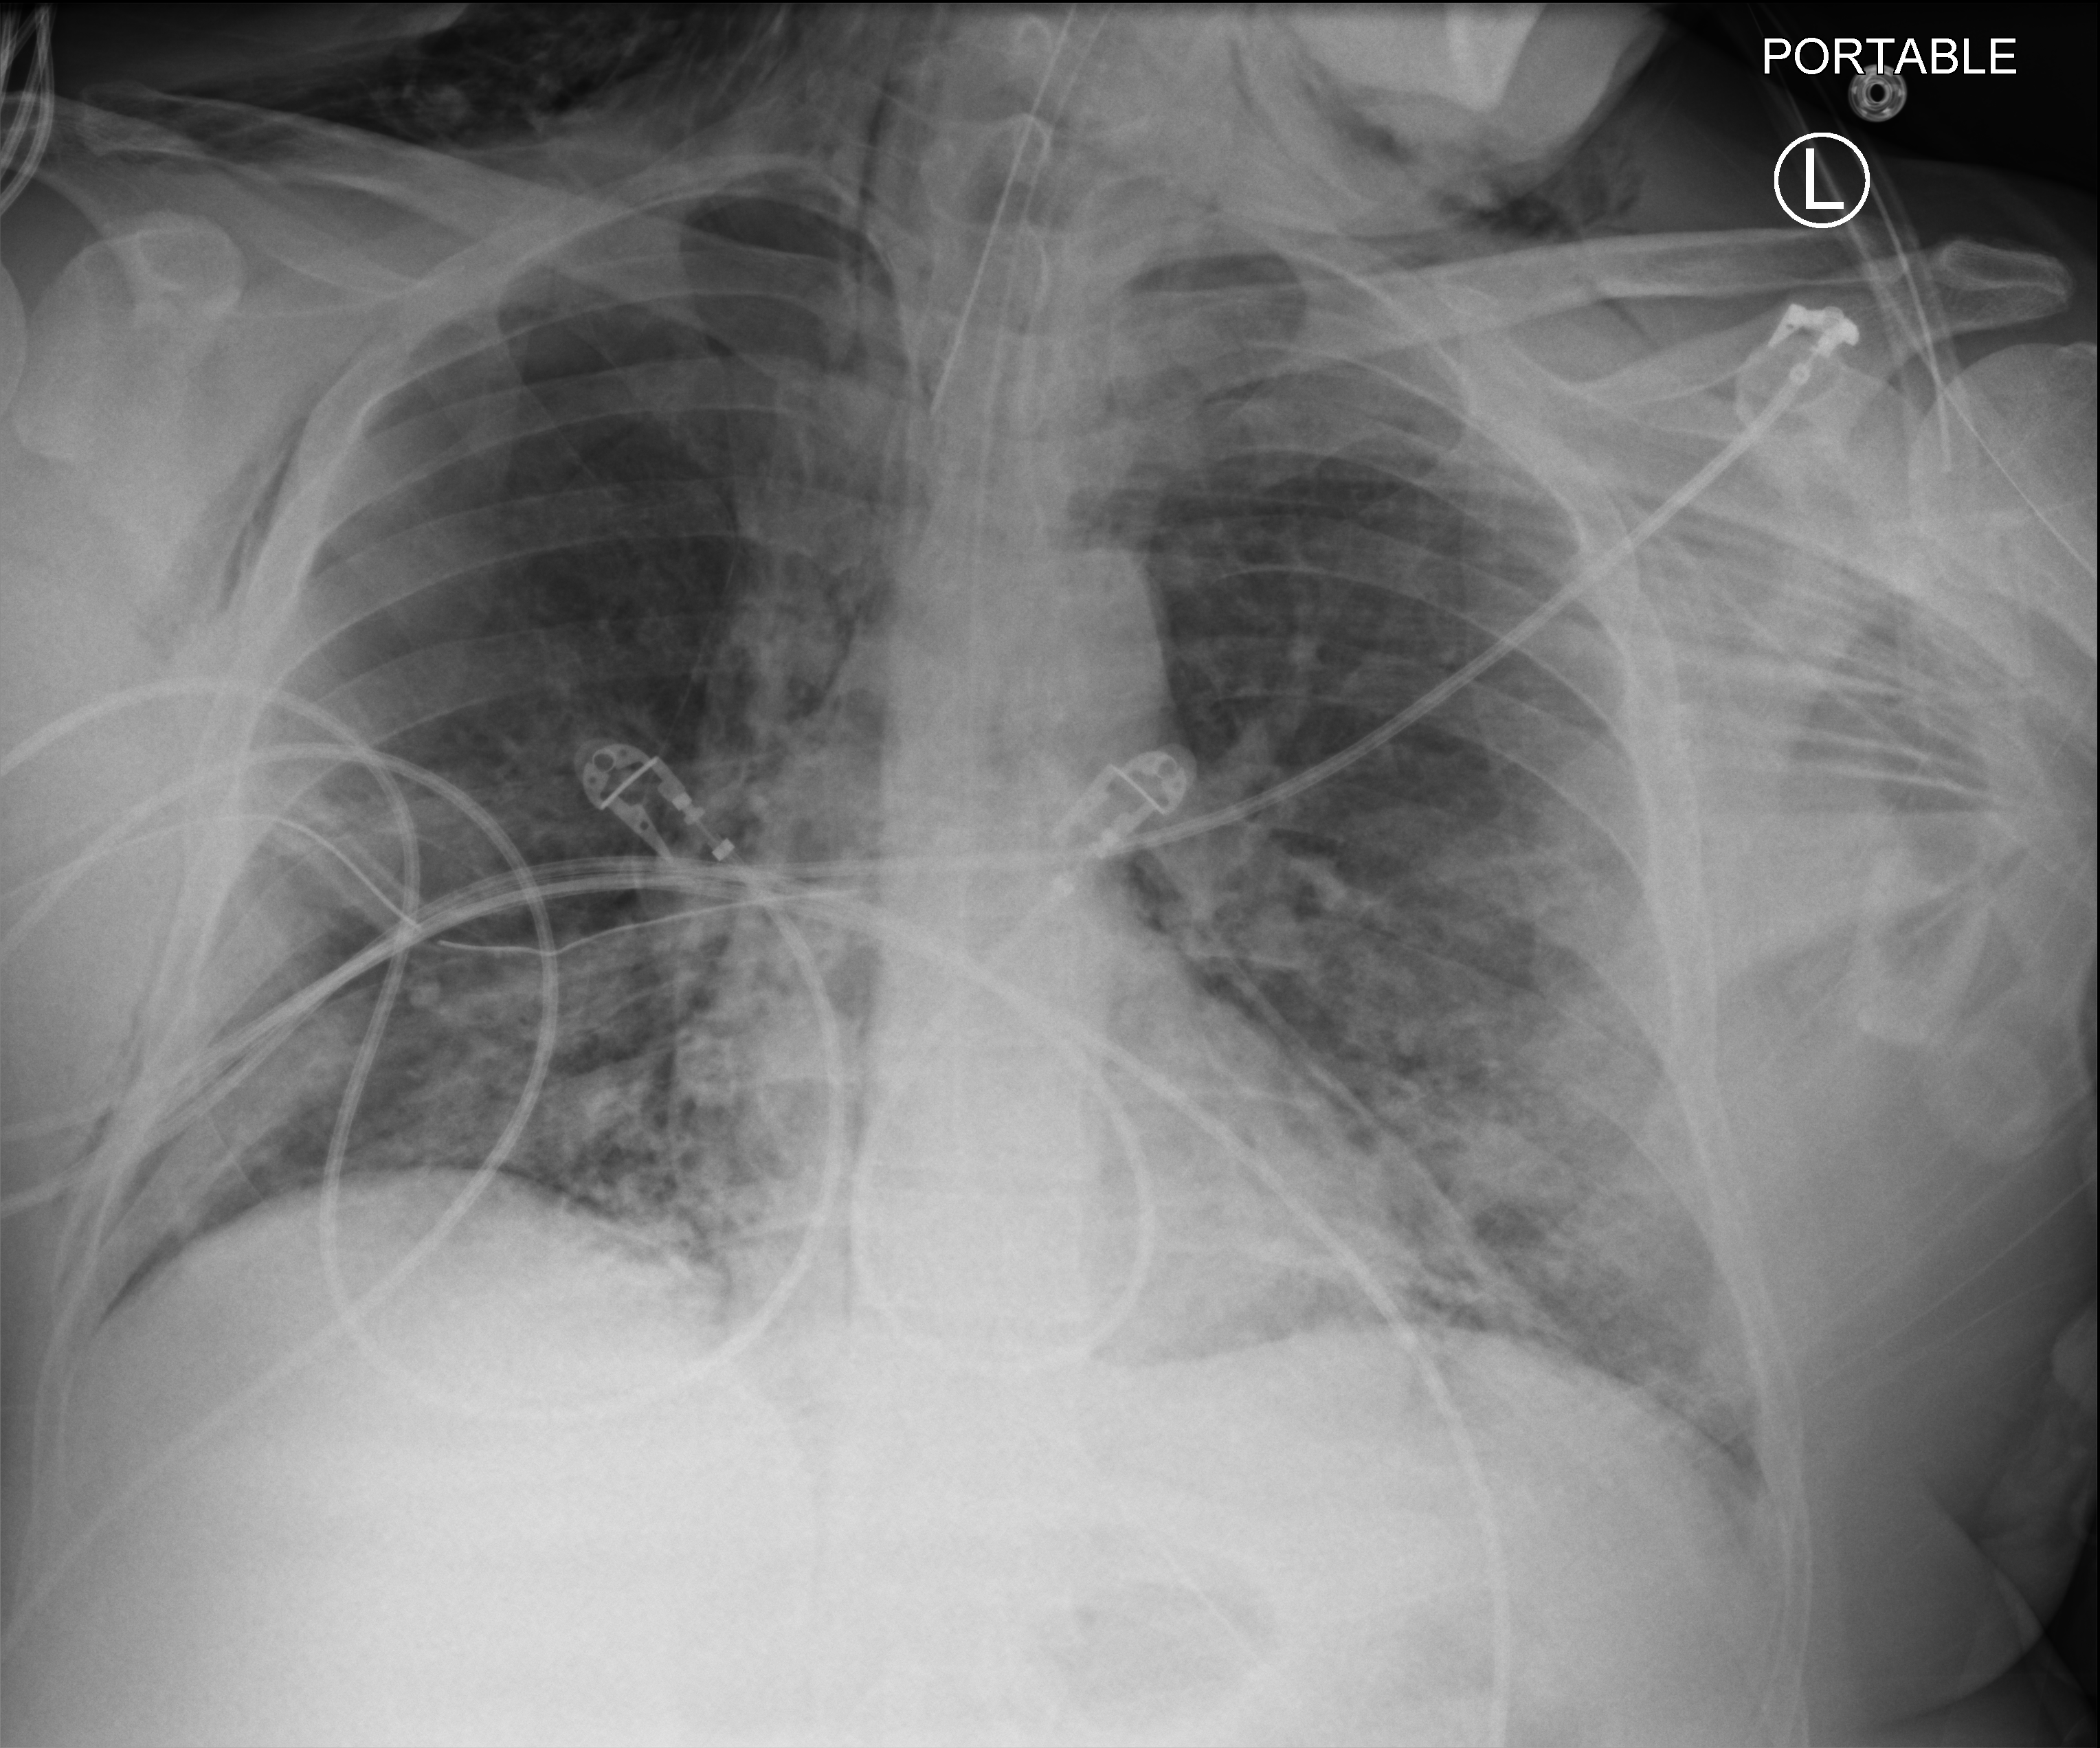
Chest X-ray (portable), anteroposterior (AP) projection. Male patient hospitalised with COVID-19, age 18–59 years.
From the hospital-stay record, not from the radiograph (when in the stay this image was taken is not recorded):
- COPD (admission record): no